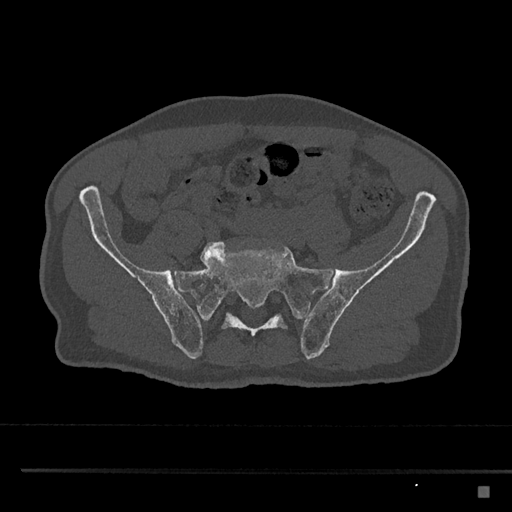
CT including the spine, one axial slice. Reconstruction kernel Br40s/3. Bone window (W 1800 / L 400 HU). 0.5 mm slice thickness. 512 × 512 image matrix, field of view 391 × 391 mm. Male patient, age 59 years. From the clinical record (not read from this slice): primary cancer: prostate.
Structures marked on this image (semi-automatically segmented with operator editing):
- L5 vertebra: bounding box [x1, y1, x2, y2] px = [200, 241, 269, 266]